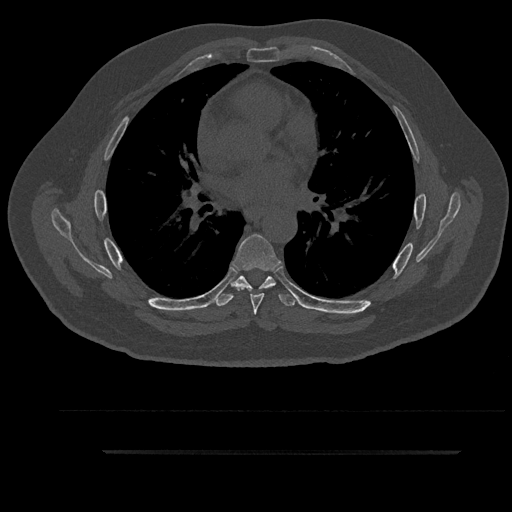
CT including the spine, one axial slice; bone window (W 1800 / L 400 HU); 512 × 512 image matrix, field of view 432 × 432 mm. Male patient, age 63 years. Case-level facts recorded for this patient, not image findings: primary cancer: renal; vertebrae with lytic lesions (as recorded): T8.
Annotated regions visible in this slice (semi-automatic segmentation, software-assisted and operator-edited):
- T5 vertebra: bounding box [x1, y1, x2, y2] px = [247, 276, 270, 291]
- T6 vertebra: [232, 234, 282, 315]
- T7 vertebra: [215, 276, 298, 306]